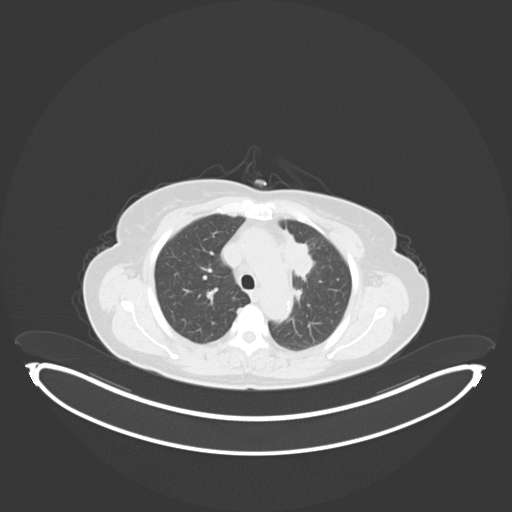
Chest CT, one axial slice; 120 kVp; lung window (W 1500 / L -600 HU); 3 mm slice thickness; 512 × 512 image matrix, field of view 500 × 500 mm. Patient: female, 65 years. From the clinical record (not read from this slice): clinical TNM (as recorded): T2a N0 M0; histopathological grade: G2-3.
Annotated regions visible in this slice (rectangle marked by the reading radiologist):
- lung tumour (recorded histology: adenocarcinoma): bounding box (x1, y1, x2, y2) in pixels: (274, 228, 316, 287)